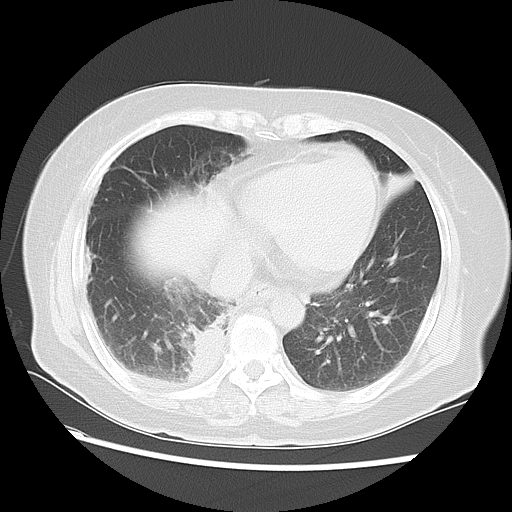
Chest CT, one axial slice. Slice 22 of 57 in the series (ordered by position). Reconstruction kernel LUNG. 120 kVp. Lung window (W 1500 / L -600 HU). 5 mm slice thickness. 512 × 512 image matrix, field of view 350 × 350 mm. Patient: female, 69 years. From the clinical record (not read from this slice): clinical TNM (as recorded): T2 N1 M1a.
Outlined on this slice (bounding box drawn by a radiologist):
- lung tumour (recorded histology: adenocarcinoma): box from (x=184, y=311) to (x=232, y=392) px